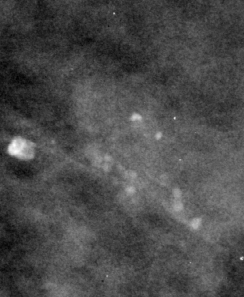
Crop from a digitized film mammogram around one marked abnormality, right breast, CC view, BI-RADS breast density category 2 (scale 1–4).
Marked abnormality: calcifications, morphology pleomorphic, distribution clustered; BI-RADS assessment category 4; pathology (as recorded): benign.